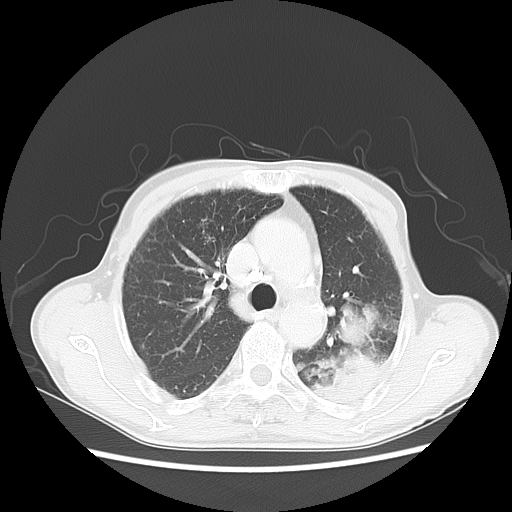
Chest CT, one axial slice. Position 37 of 51 along the scan axis. Reconstruction kernel LUNG. 120 kVp. Lung window (W 1500 / L -600 HU). 5 mm slice thickness. 512 × 512 image matrix. Patient: male, 64 years. Case-level facts recorded for this patient, not image findings: clinical TNM (as recorded): T4 N0 M0.
Annotated regions visible in this slice (rectangle marked by the reading radiologist):
- lung tumour (recorded histology: squamous cell carcinoma): bounding box <325,291,384,410> (left, top, right, bottom; pixels)